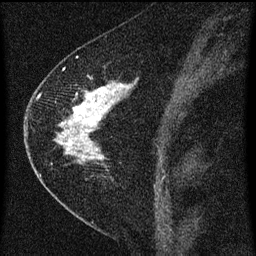
Breast MRI (dynamic contrast-enhanced), one sagittal slice; position 33 of 60 along the scan axis; dynamic contrast-enhanced series, image 2 of 3 at this slice position (ordered by acquisition); 1.5 T; TE 4.2 ms, TR 8 ms; 256 × 256 image matrix, field of view 180 × 180 mm. Female patient, age 47 years.
Structures marked on this image (semi-automatic segmentation, software-assisted and operator-edited):
- analysis volume of interest (the breast-tissue region the enhancement analysis was run in; not a lesion): box from (x=38, y=76) to (x=135, y=193) px
- tumour enhancement mask (voxels above the 70 % enhancement threshold inside the analysis volume of interest): (x=58, y=84)–(x=131, y=161)